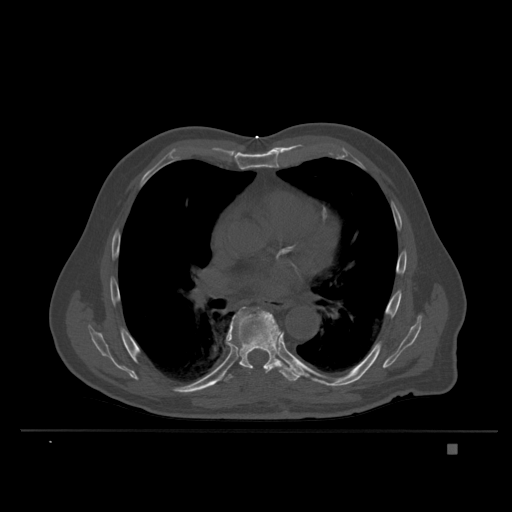
CT including the spine, one axial slice; slice 236 of 435 in the series (ordered by position); bone window (W 1800 / L 400 HU); 1.5 mm slice thickness; 512 × 512 image matrix. Patient: male, 73 years. From the clinical record (not read from this slice): primary cancer: skin.
Outlined on this slice (semi-automatic segmentation, software-assisted and operator-edited):
- T7 vertebra: bounding box <226,307,283,373> (left, top, right, bottom; pixels)
- T8 vertebra: <224,308,301,382>